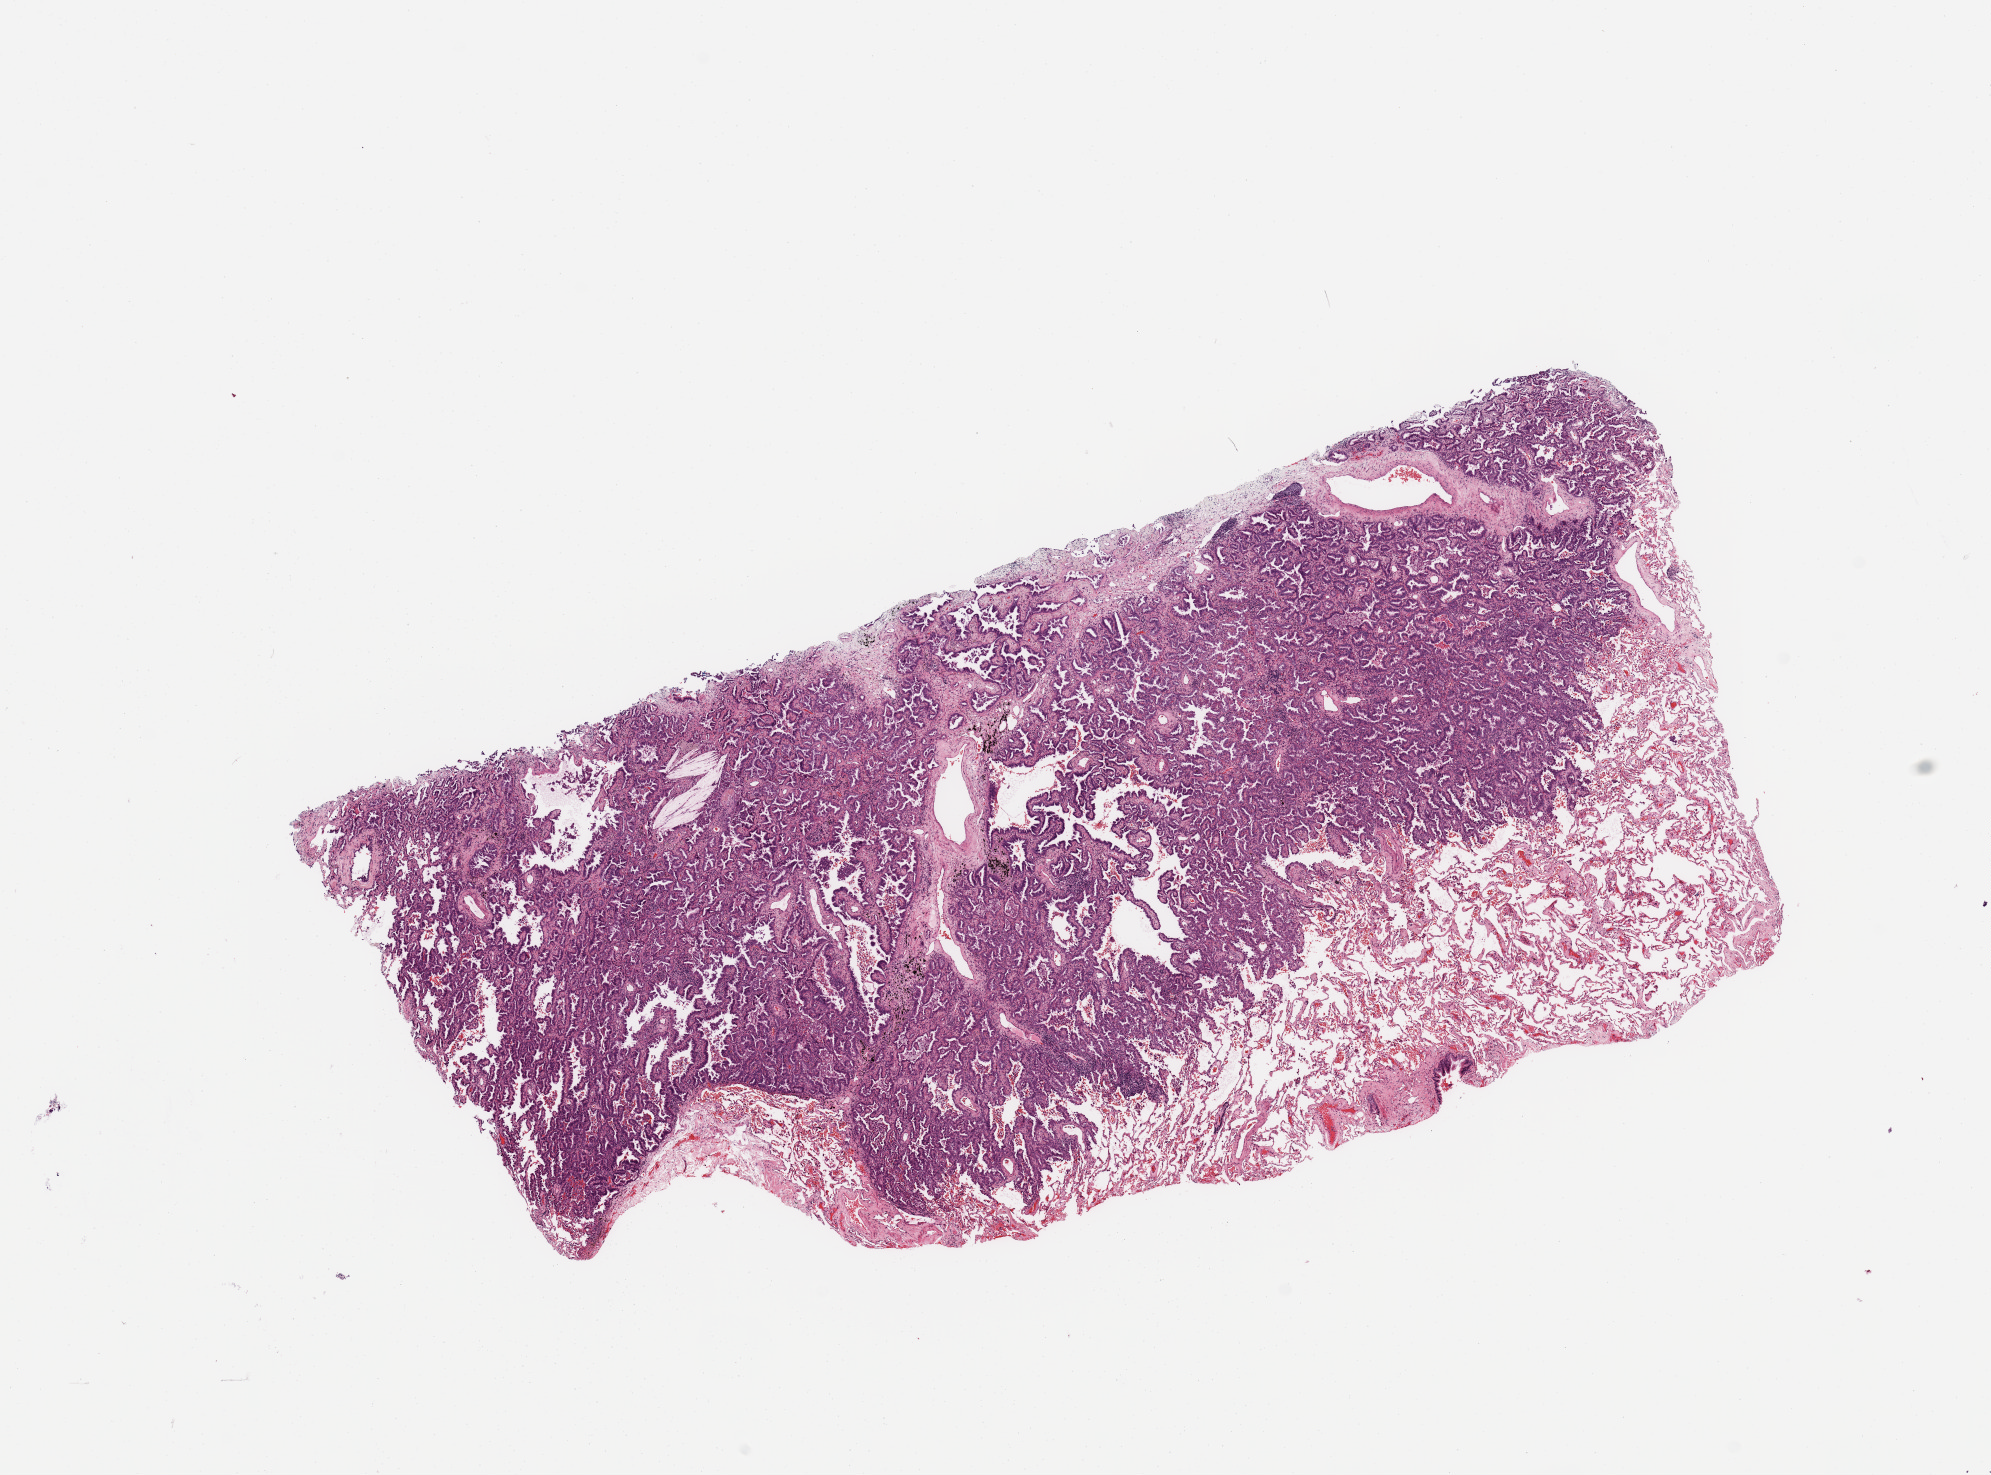
H&E-stained whole-slide image — low-resolution overview of the scanned area, about 15.8 x 11.7 mm (from a 20x scan), tumour tissue sample, lung. Patient: female, age 67 years. Histologic grade: G1 (well differentiated).
* AJCC pathologic stage: IA
* primary tumour site (as recorded): left upper lobe
* histologic diagnosis: Adenocarcinoma, NOS